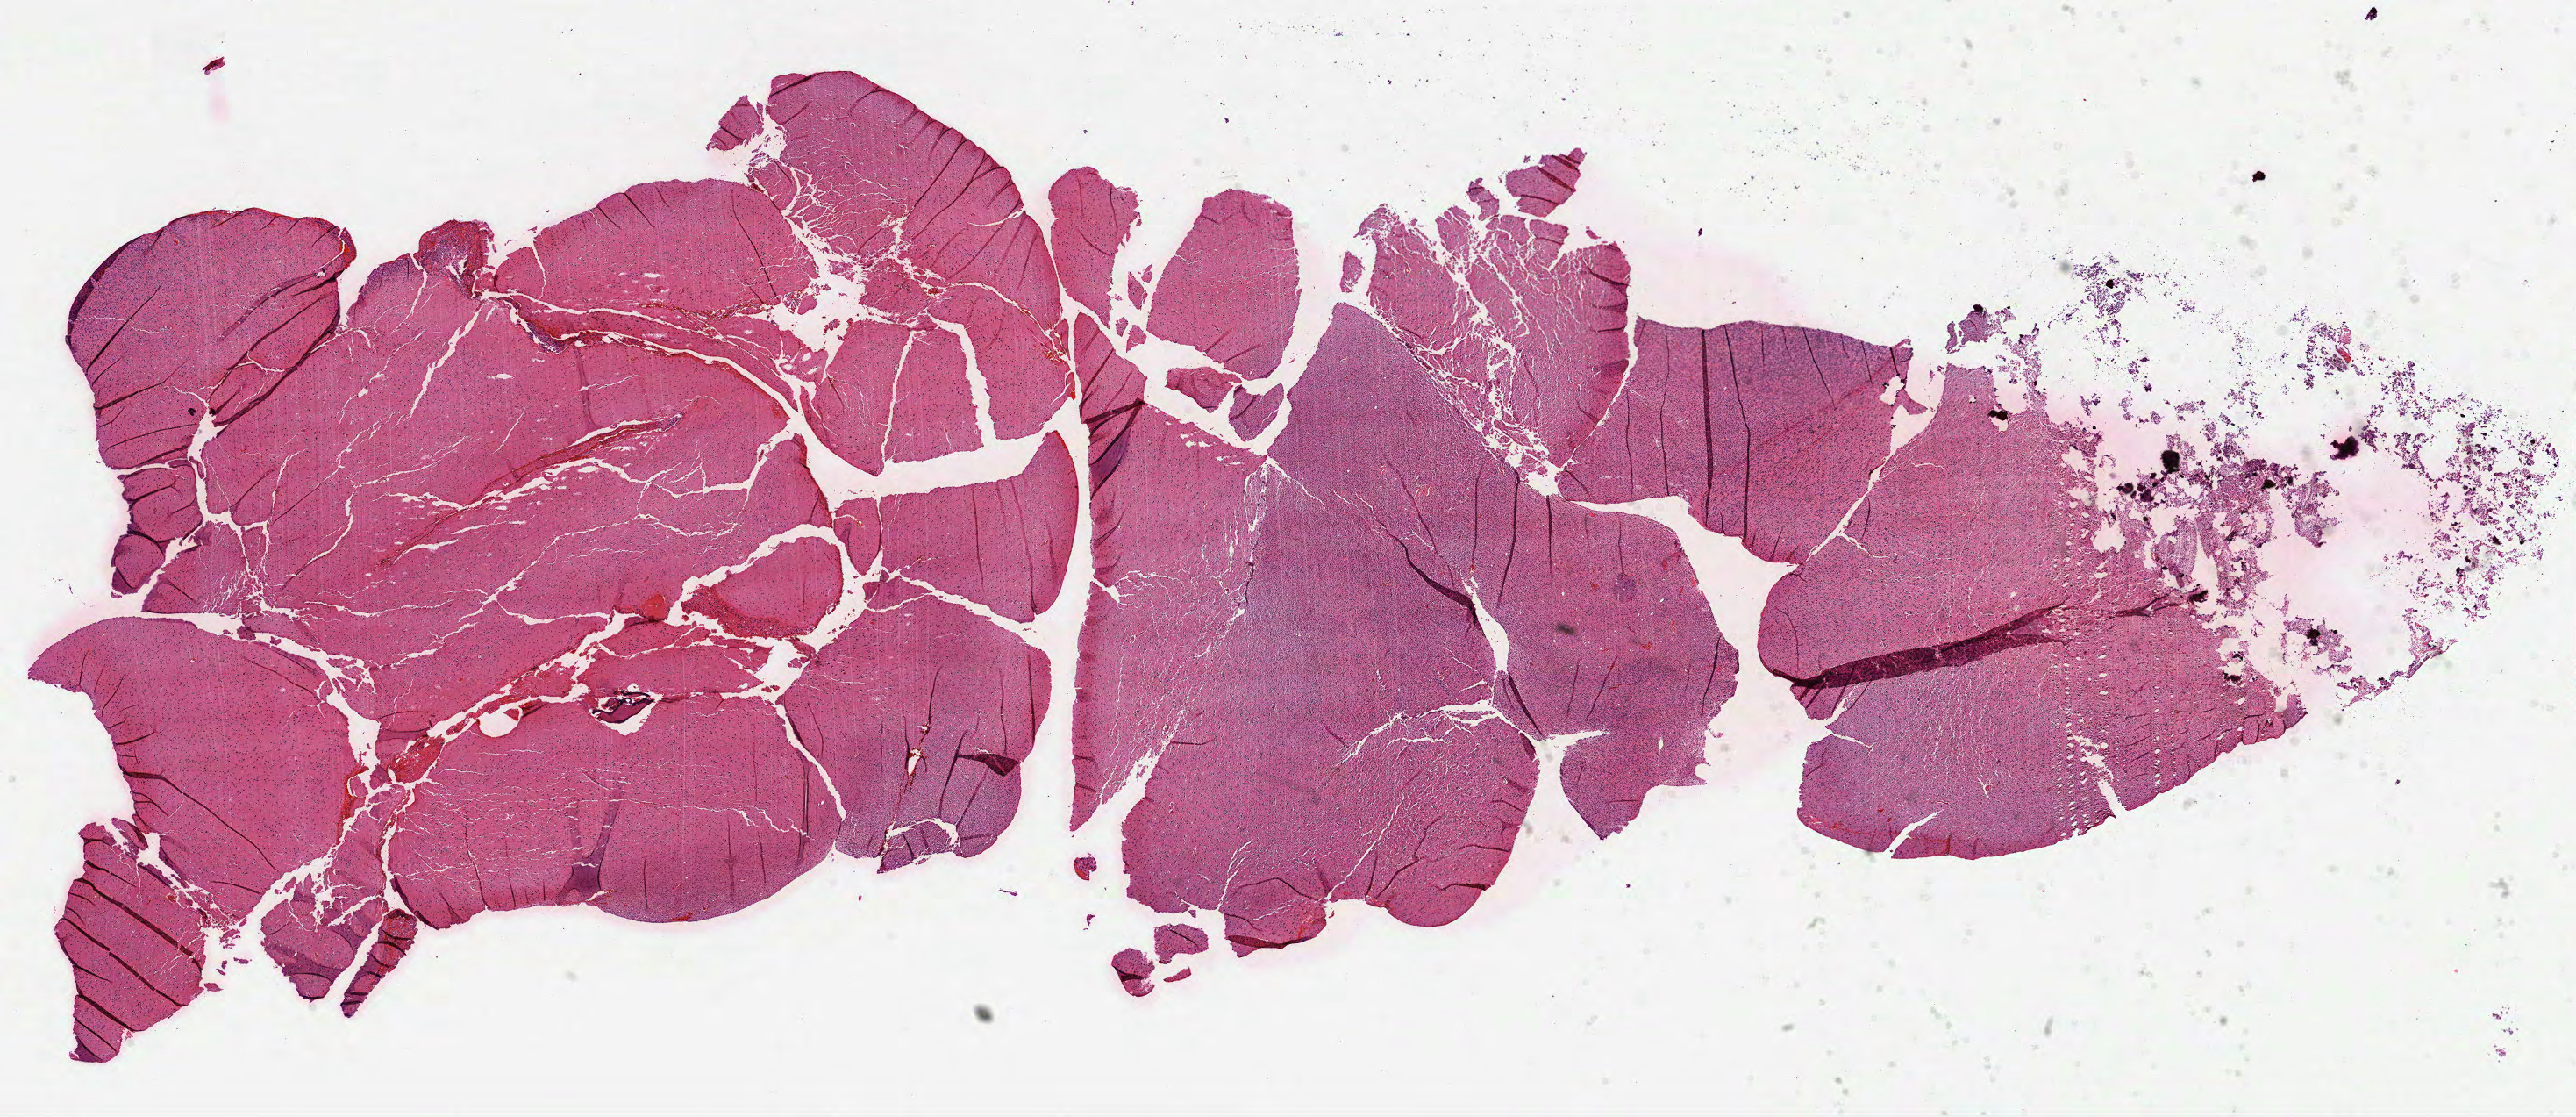
H&E whole-slide image — whole scanned area (about 23.7 x 10.3 mm) shown as a low-resolution overview; formalin-fixed paraffin-embedded (FFPE) diagnostic section; brain, primary tumour sample. Female patient; age at initial diagnosis 53 years. Histologic grade: G3 (poorly differentiated).
- pathologic diagnosis: Oligodendroglioma, anaplastic
- laterality: right